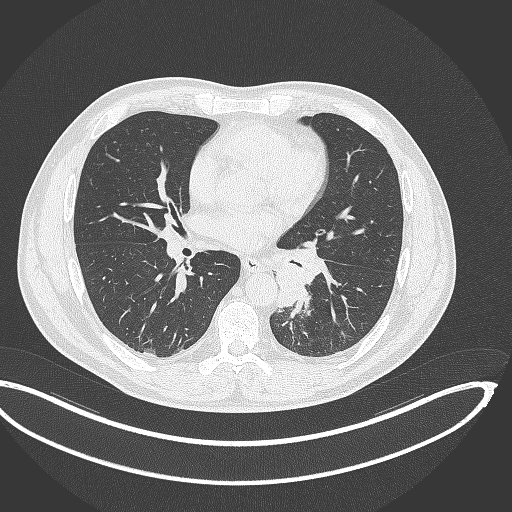
Chest CT, one axial slice. Reconstruction kernel B70f. 120 kVp. Lung window (W 1500 / L -600 HU). 1 mm slice thickness. 512 × 512 image matrix, field of view 442 × 442 mm. Patient: male, 50 years. From the clinical record (not read from this slice): clinical TNM (as recorded): T2a N3 M0.
Annotated regions visible in this slice (bounding box drawn by a radiologist):
- lung tumour (recorded histology: squamous cell carcinoma): bounding box <271,237,329,311> (left, top, right, bottom; pixels)